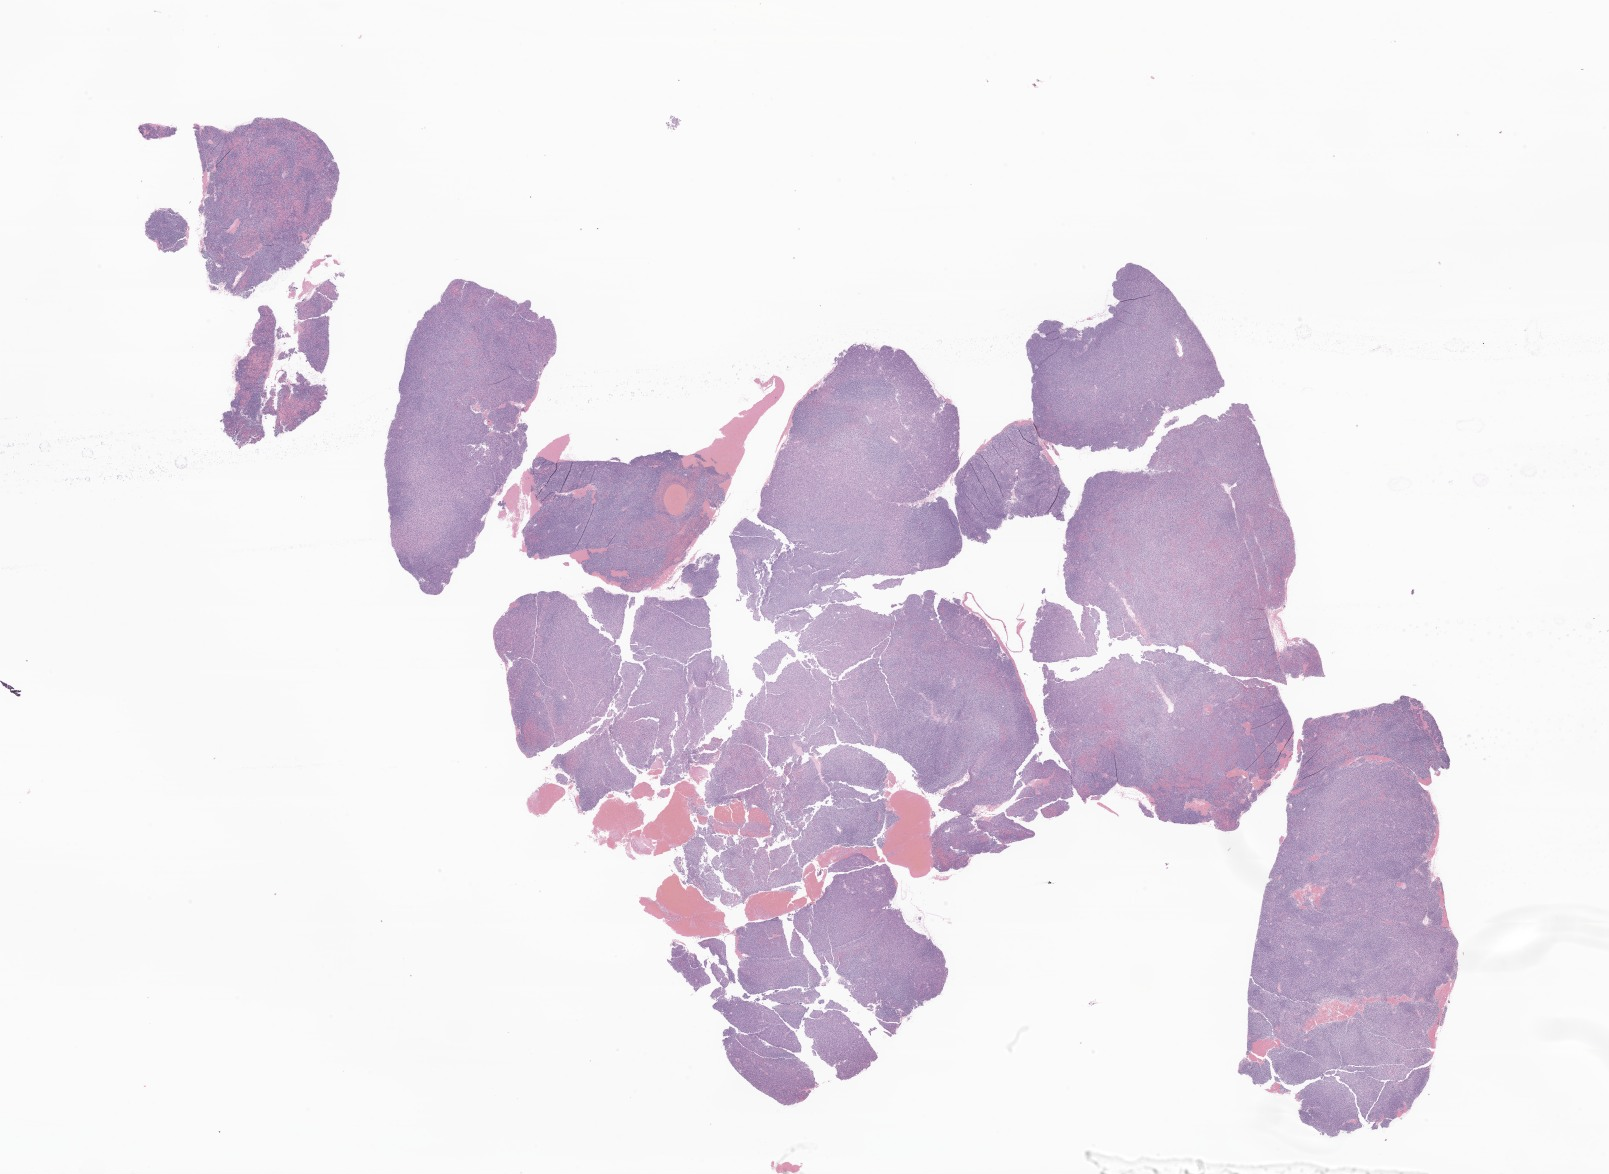
Hematoxylin and eosin (H&E) whole-slide image of tumor tissue from the brain, low-resolution overview of the scanned area, about 27.1 x 19.8 mm; formalin-fixed paraffin-embedded section. Patient male; age 171 months (14 years 3 months).
Diagnosis (ICD-O-3 morphology term): Glioma, malignant.